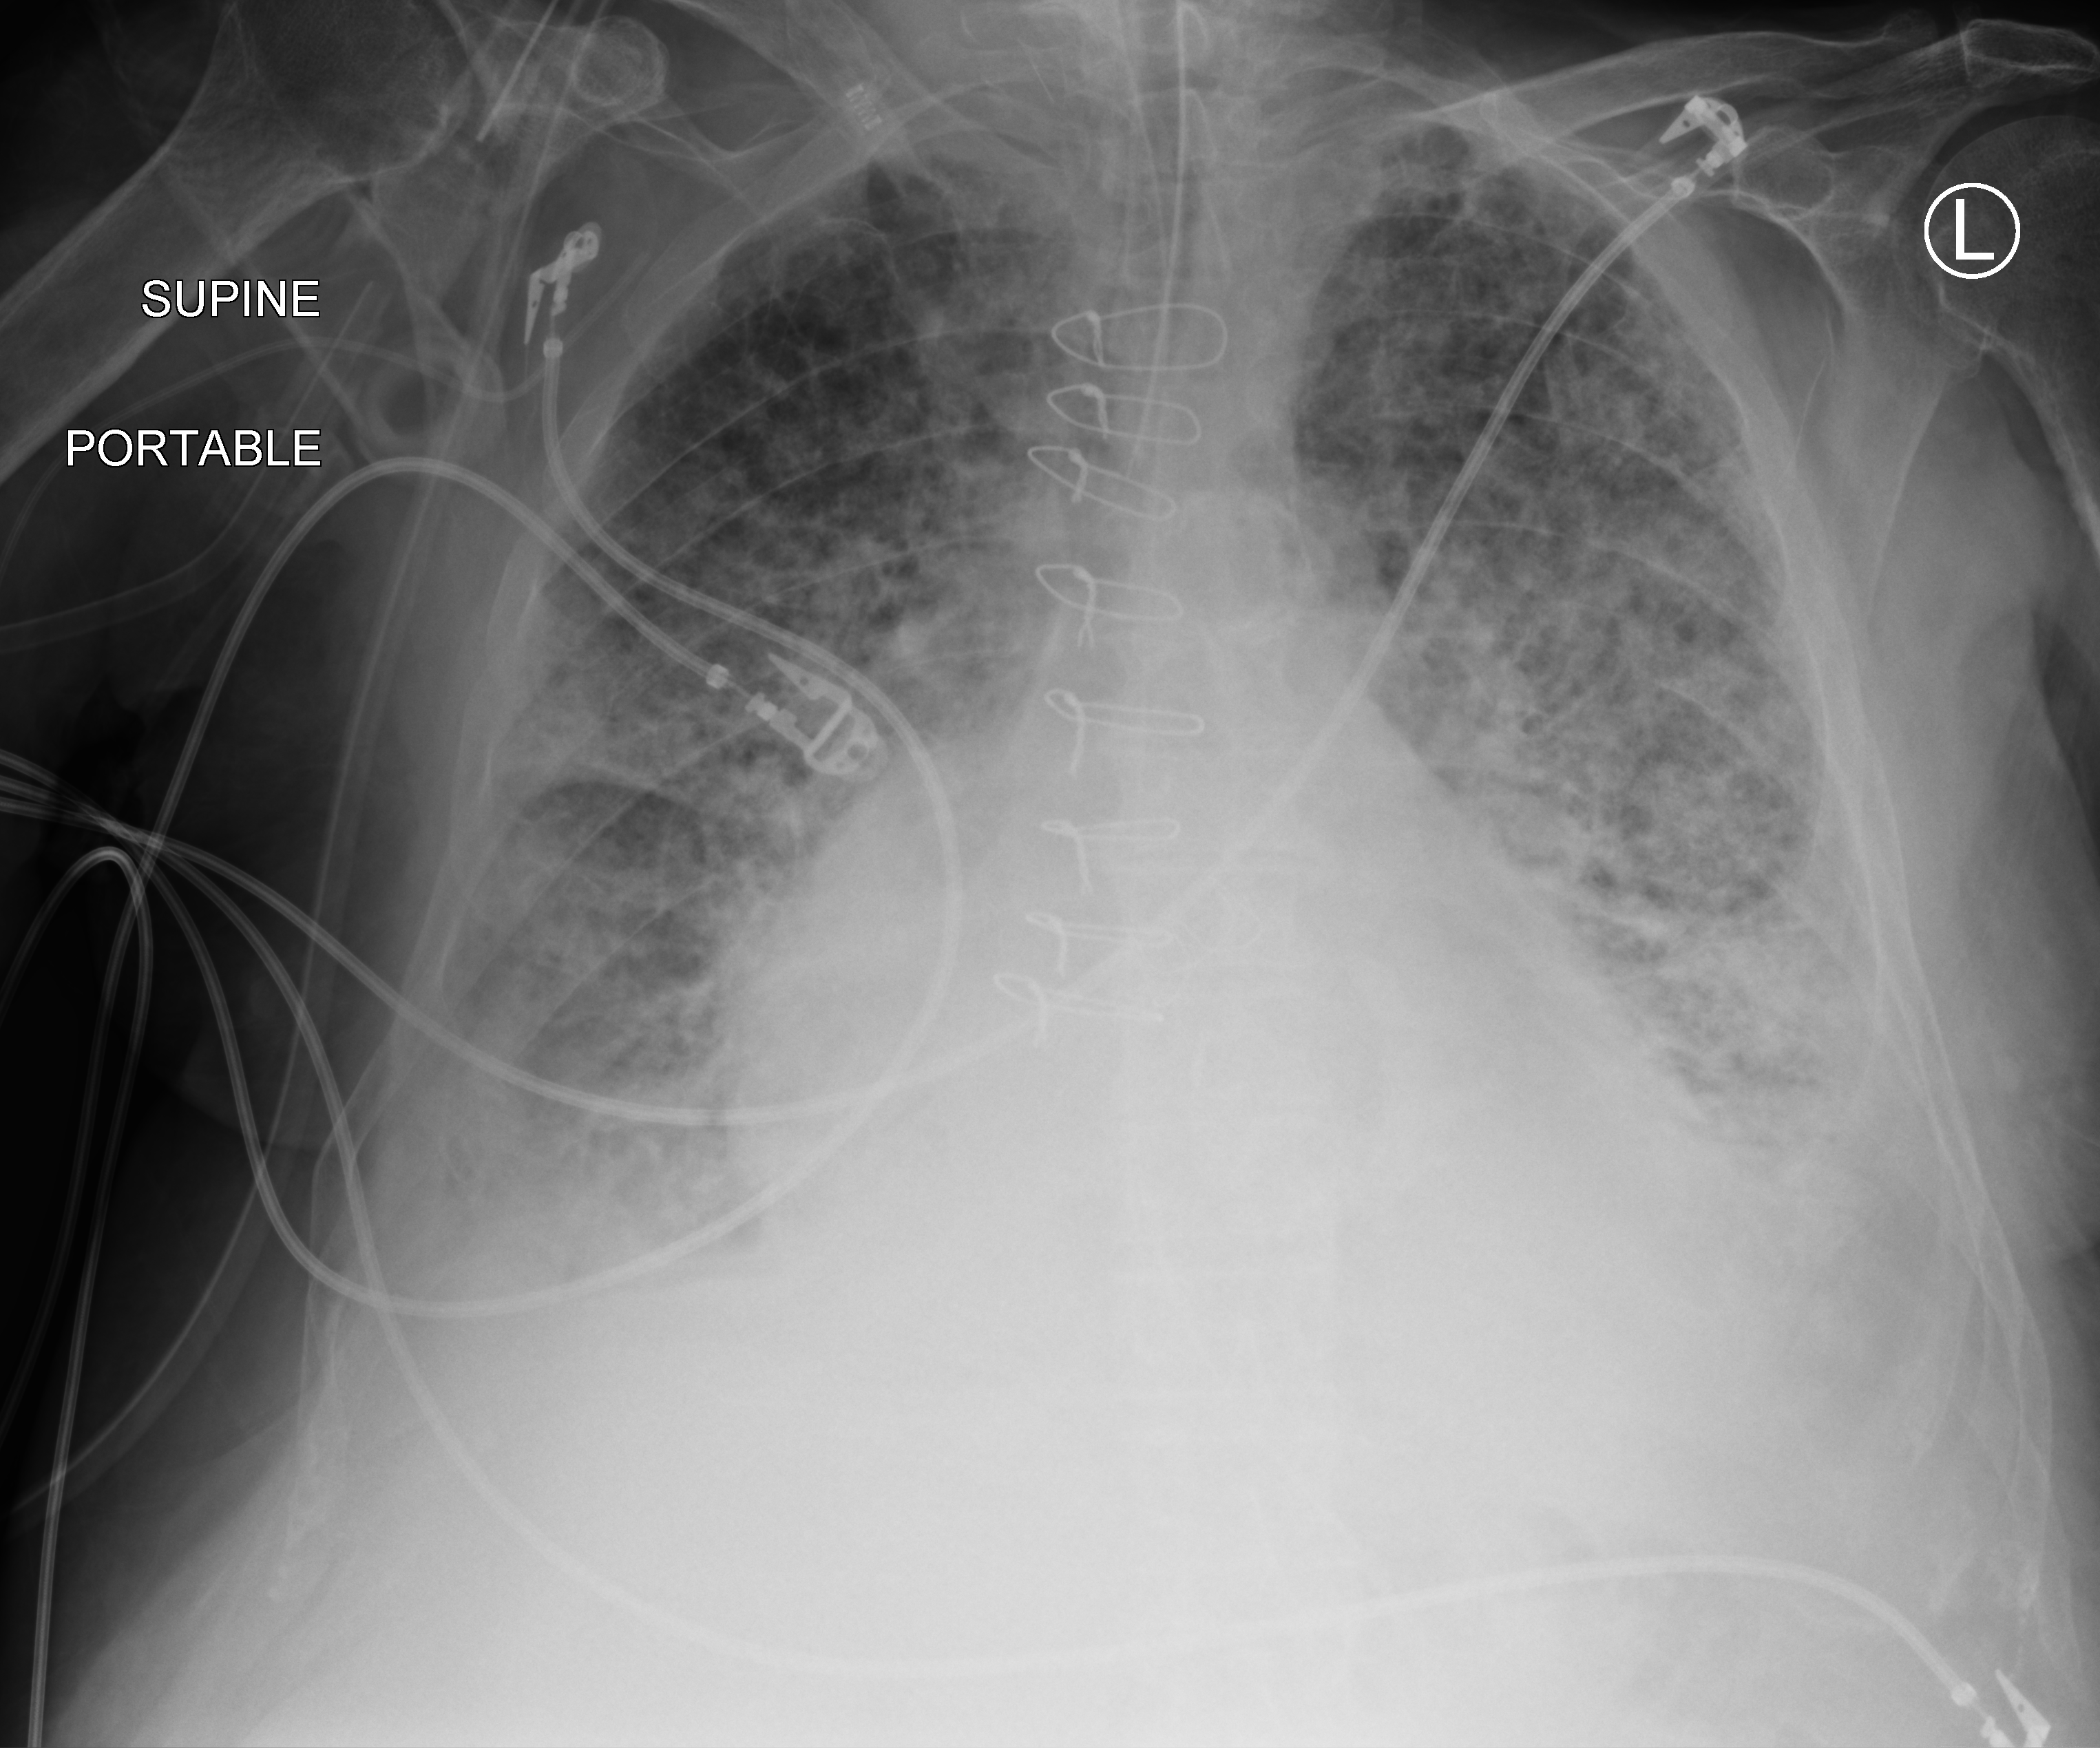
Portable chest radiograph, anteroposterior (AP) projection. Male patient hospitalised with COVID-19, age 75–90 years.
Admission-level facts for this patient (not findings on this image; timing relative to this image not recorded): admitted to intensive care during this hospital stay: yes.